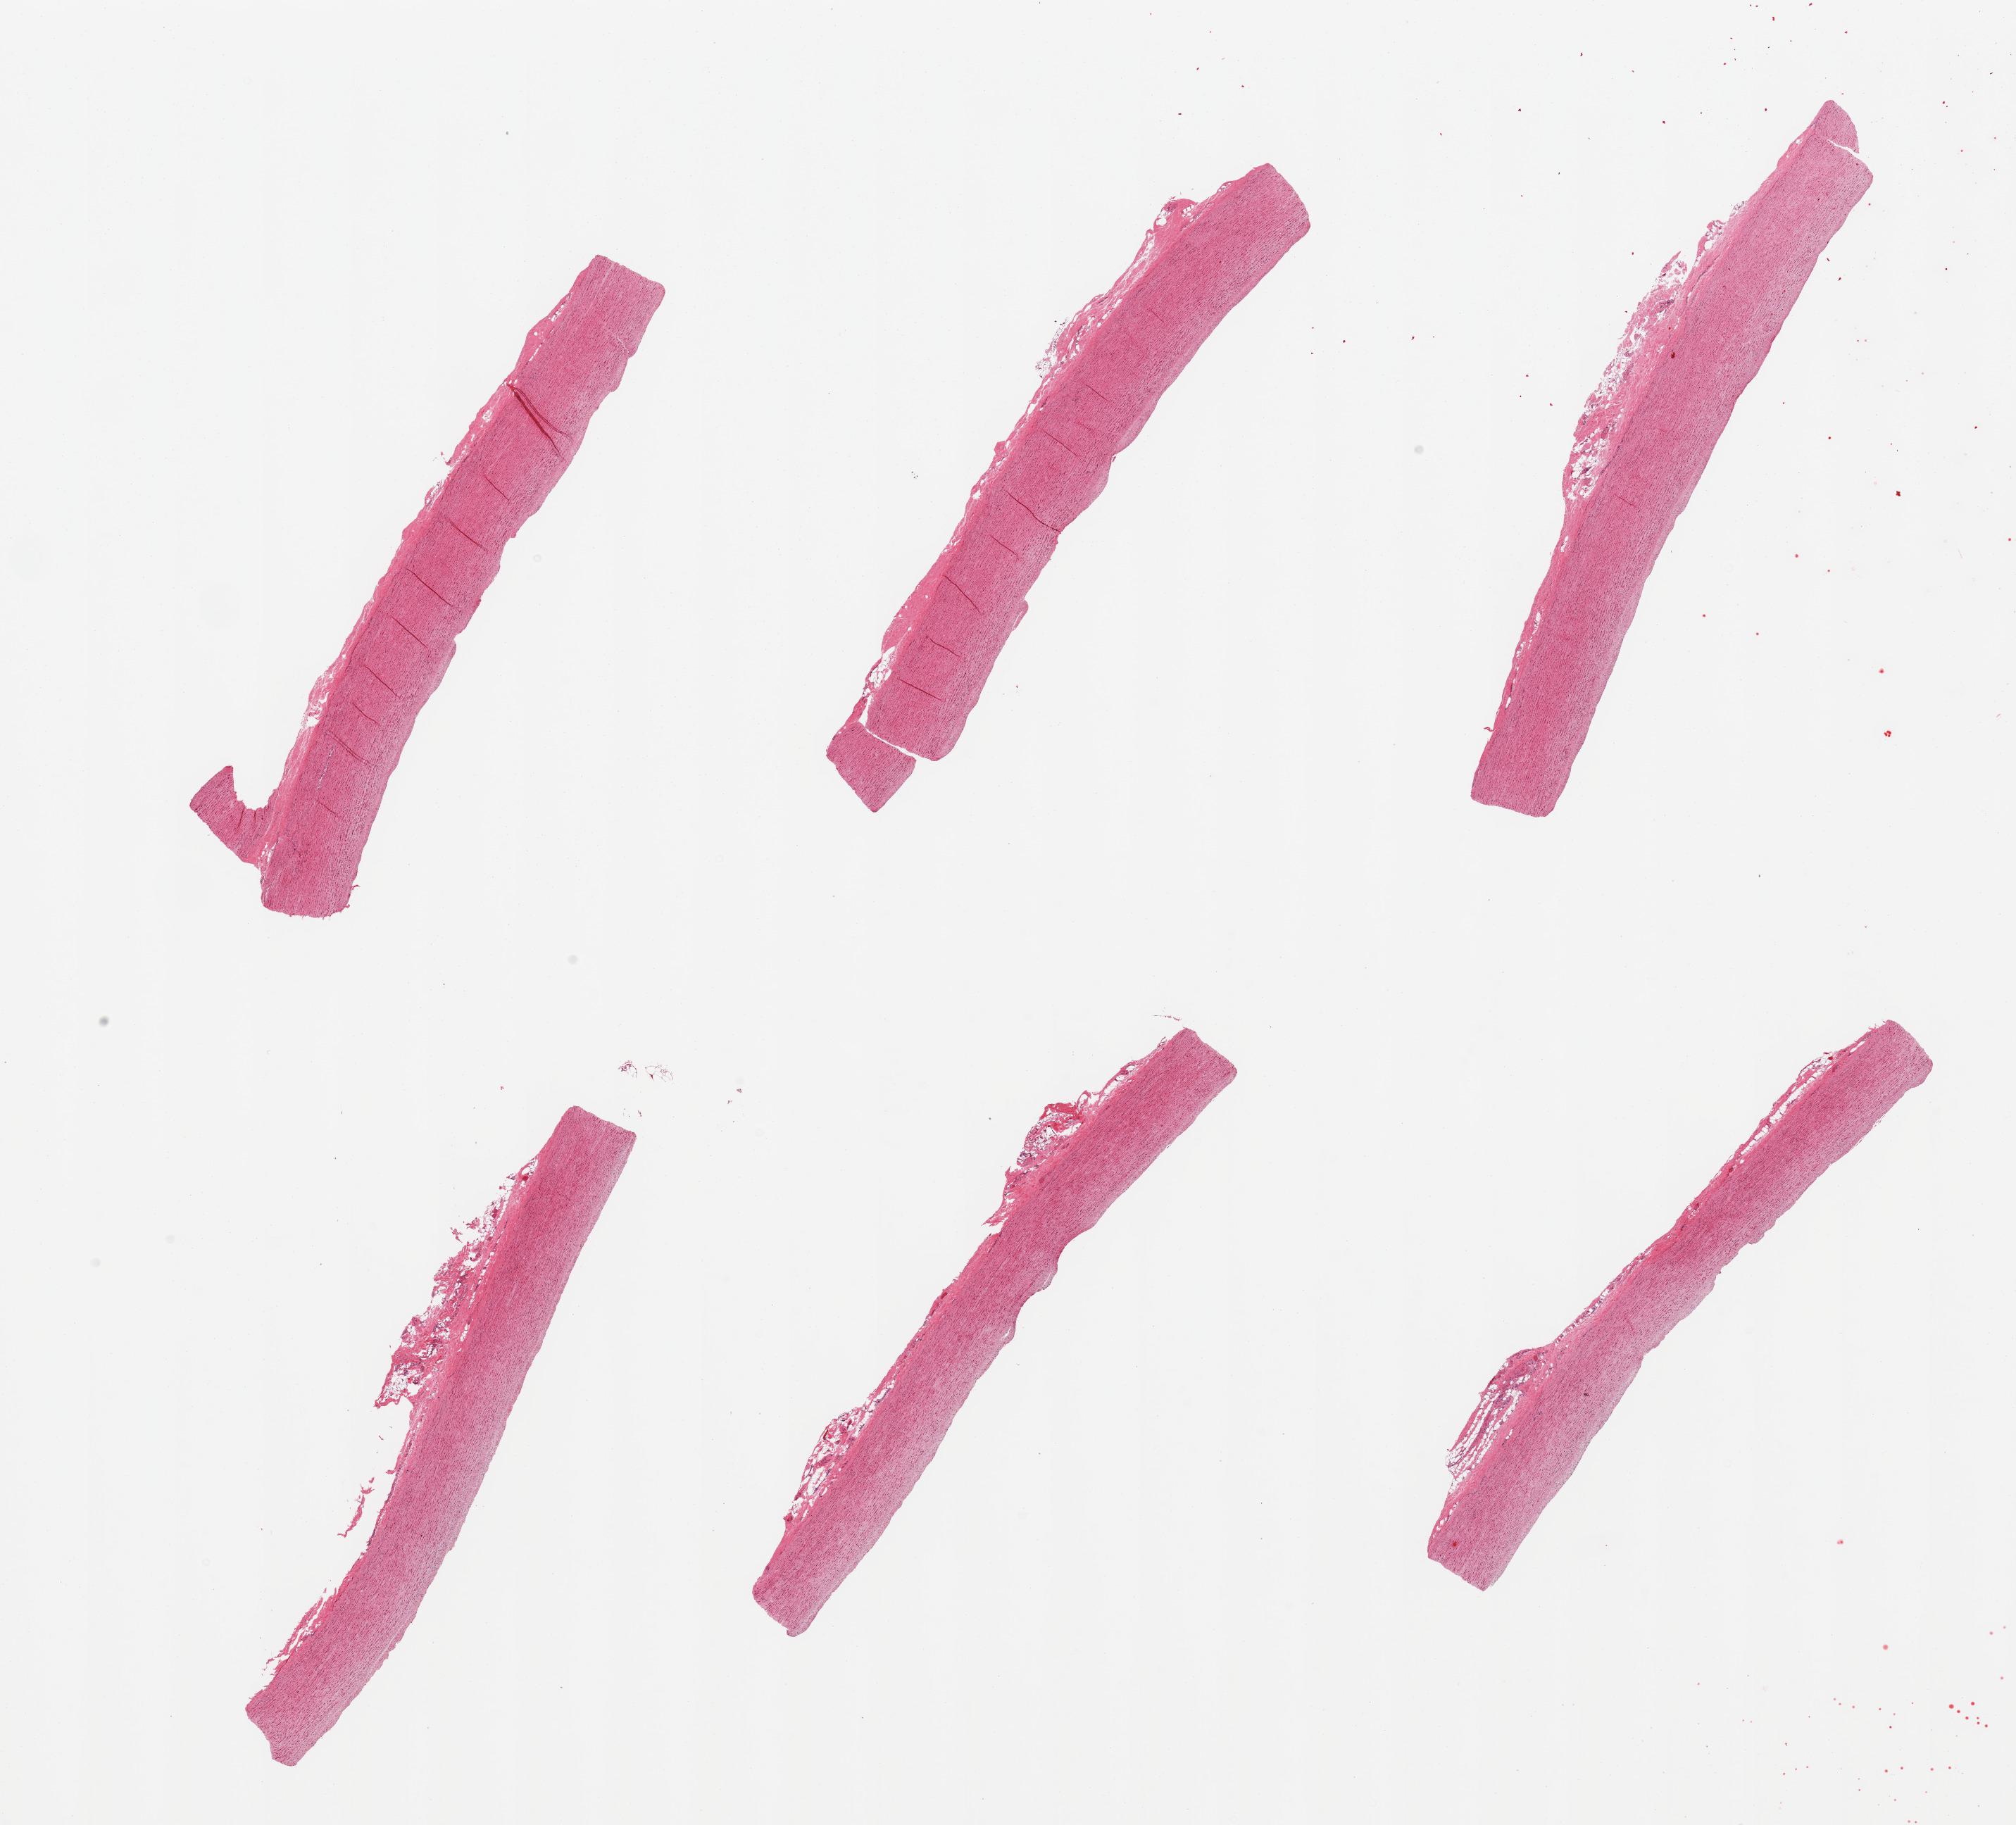
H&E whole-slide image, low-resolution overview of the scanned area, about 22.6 x 20.5 mm (acquisition: 20x scan). PAXgene-fixed paraffin-embedded (PFPE) section. Target tissue: aorta. Tissue donor sample. Male donor.
Review note (as recorded): 6 pieces, minimal atherosis.